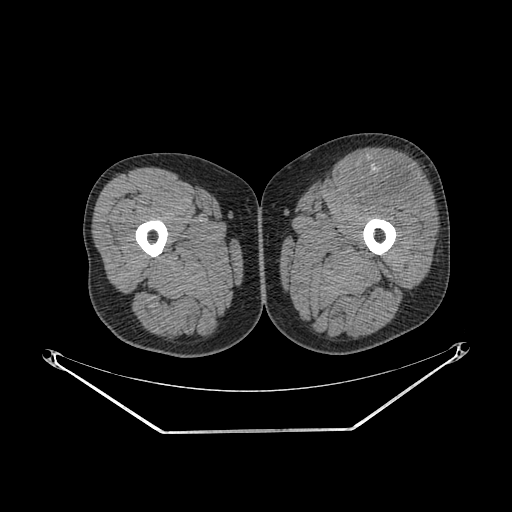
CT of an extremity soft-tissue mass (from a PET/CT study), one axial slice; position 232 of 267 along the scan axis; 140 kVp; soft-tissue window (W 400 / L 40 HU); 3.75 mm slice thickness; 512 × 512 image matrix, field of view 500 × 500 mm. Male patient. Case-level facts recorded for this patient, not image findings: histological type: extraskeletal osteosarcoma; grade: high; site of the primary tumour: thigh.
Outlined on this slice (expert contour drawn on MRI and transferred to this co-registered scan by the dataset authors):
- gross tumour volume (mass): bounding box <356,160,428,211> (left, top, right, bottom; pixels)